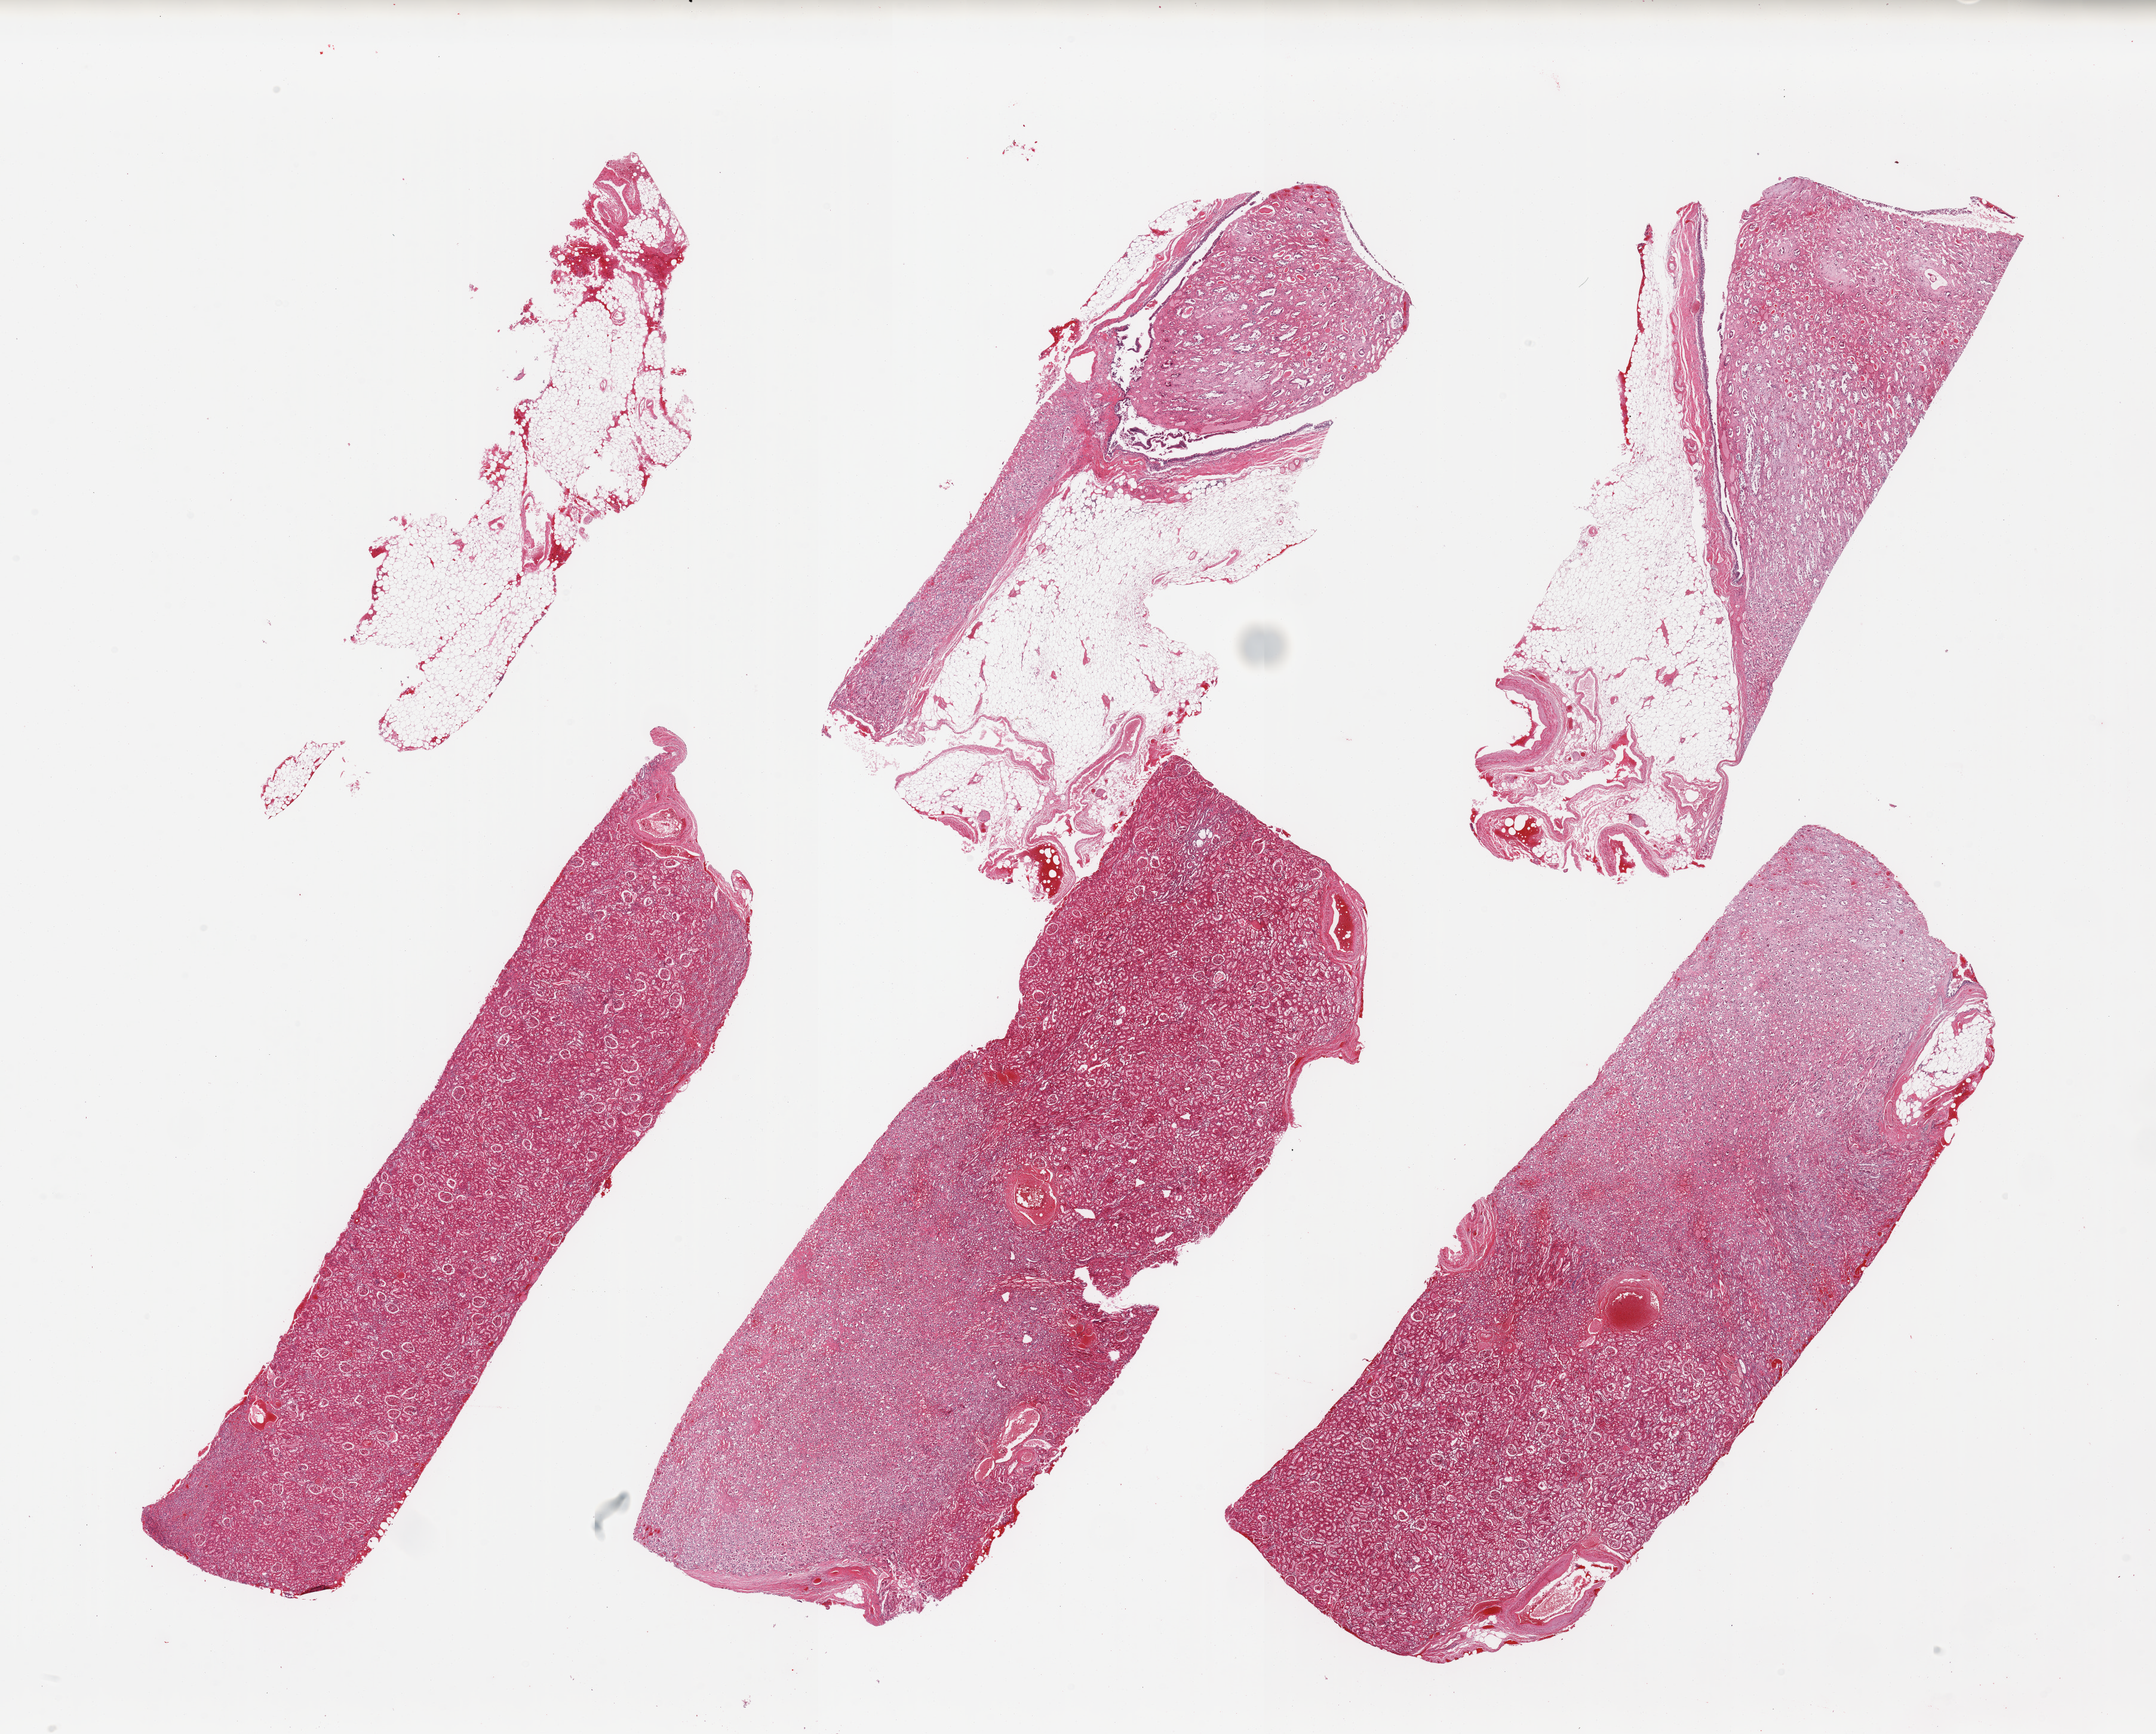
Digitized hematoxylin and eosin (H&E)-stained section, shown as a low-resolution overview of the whole scanned area (about 28.5 x 23.0 mm), PAXgene-fixed, paraffin-embedded tissue, sampled site (target tissue): renal cortex, tissue donor sample. Female donor.
- reviewer comment on this tissue sample: 6 pieces, ~30% adherent fat; glomeruli present, advanced tubular autolysis